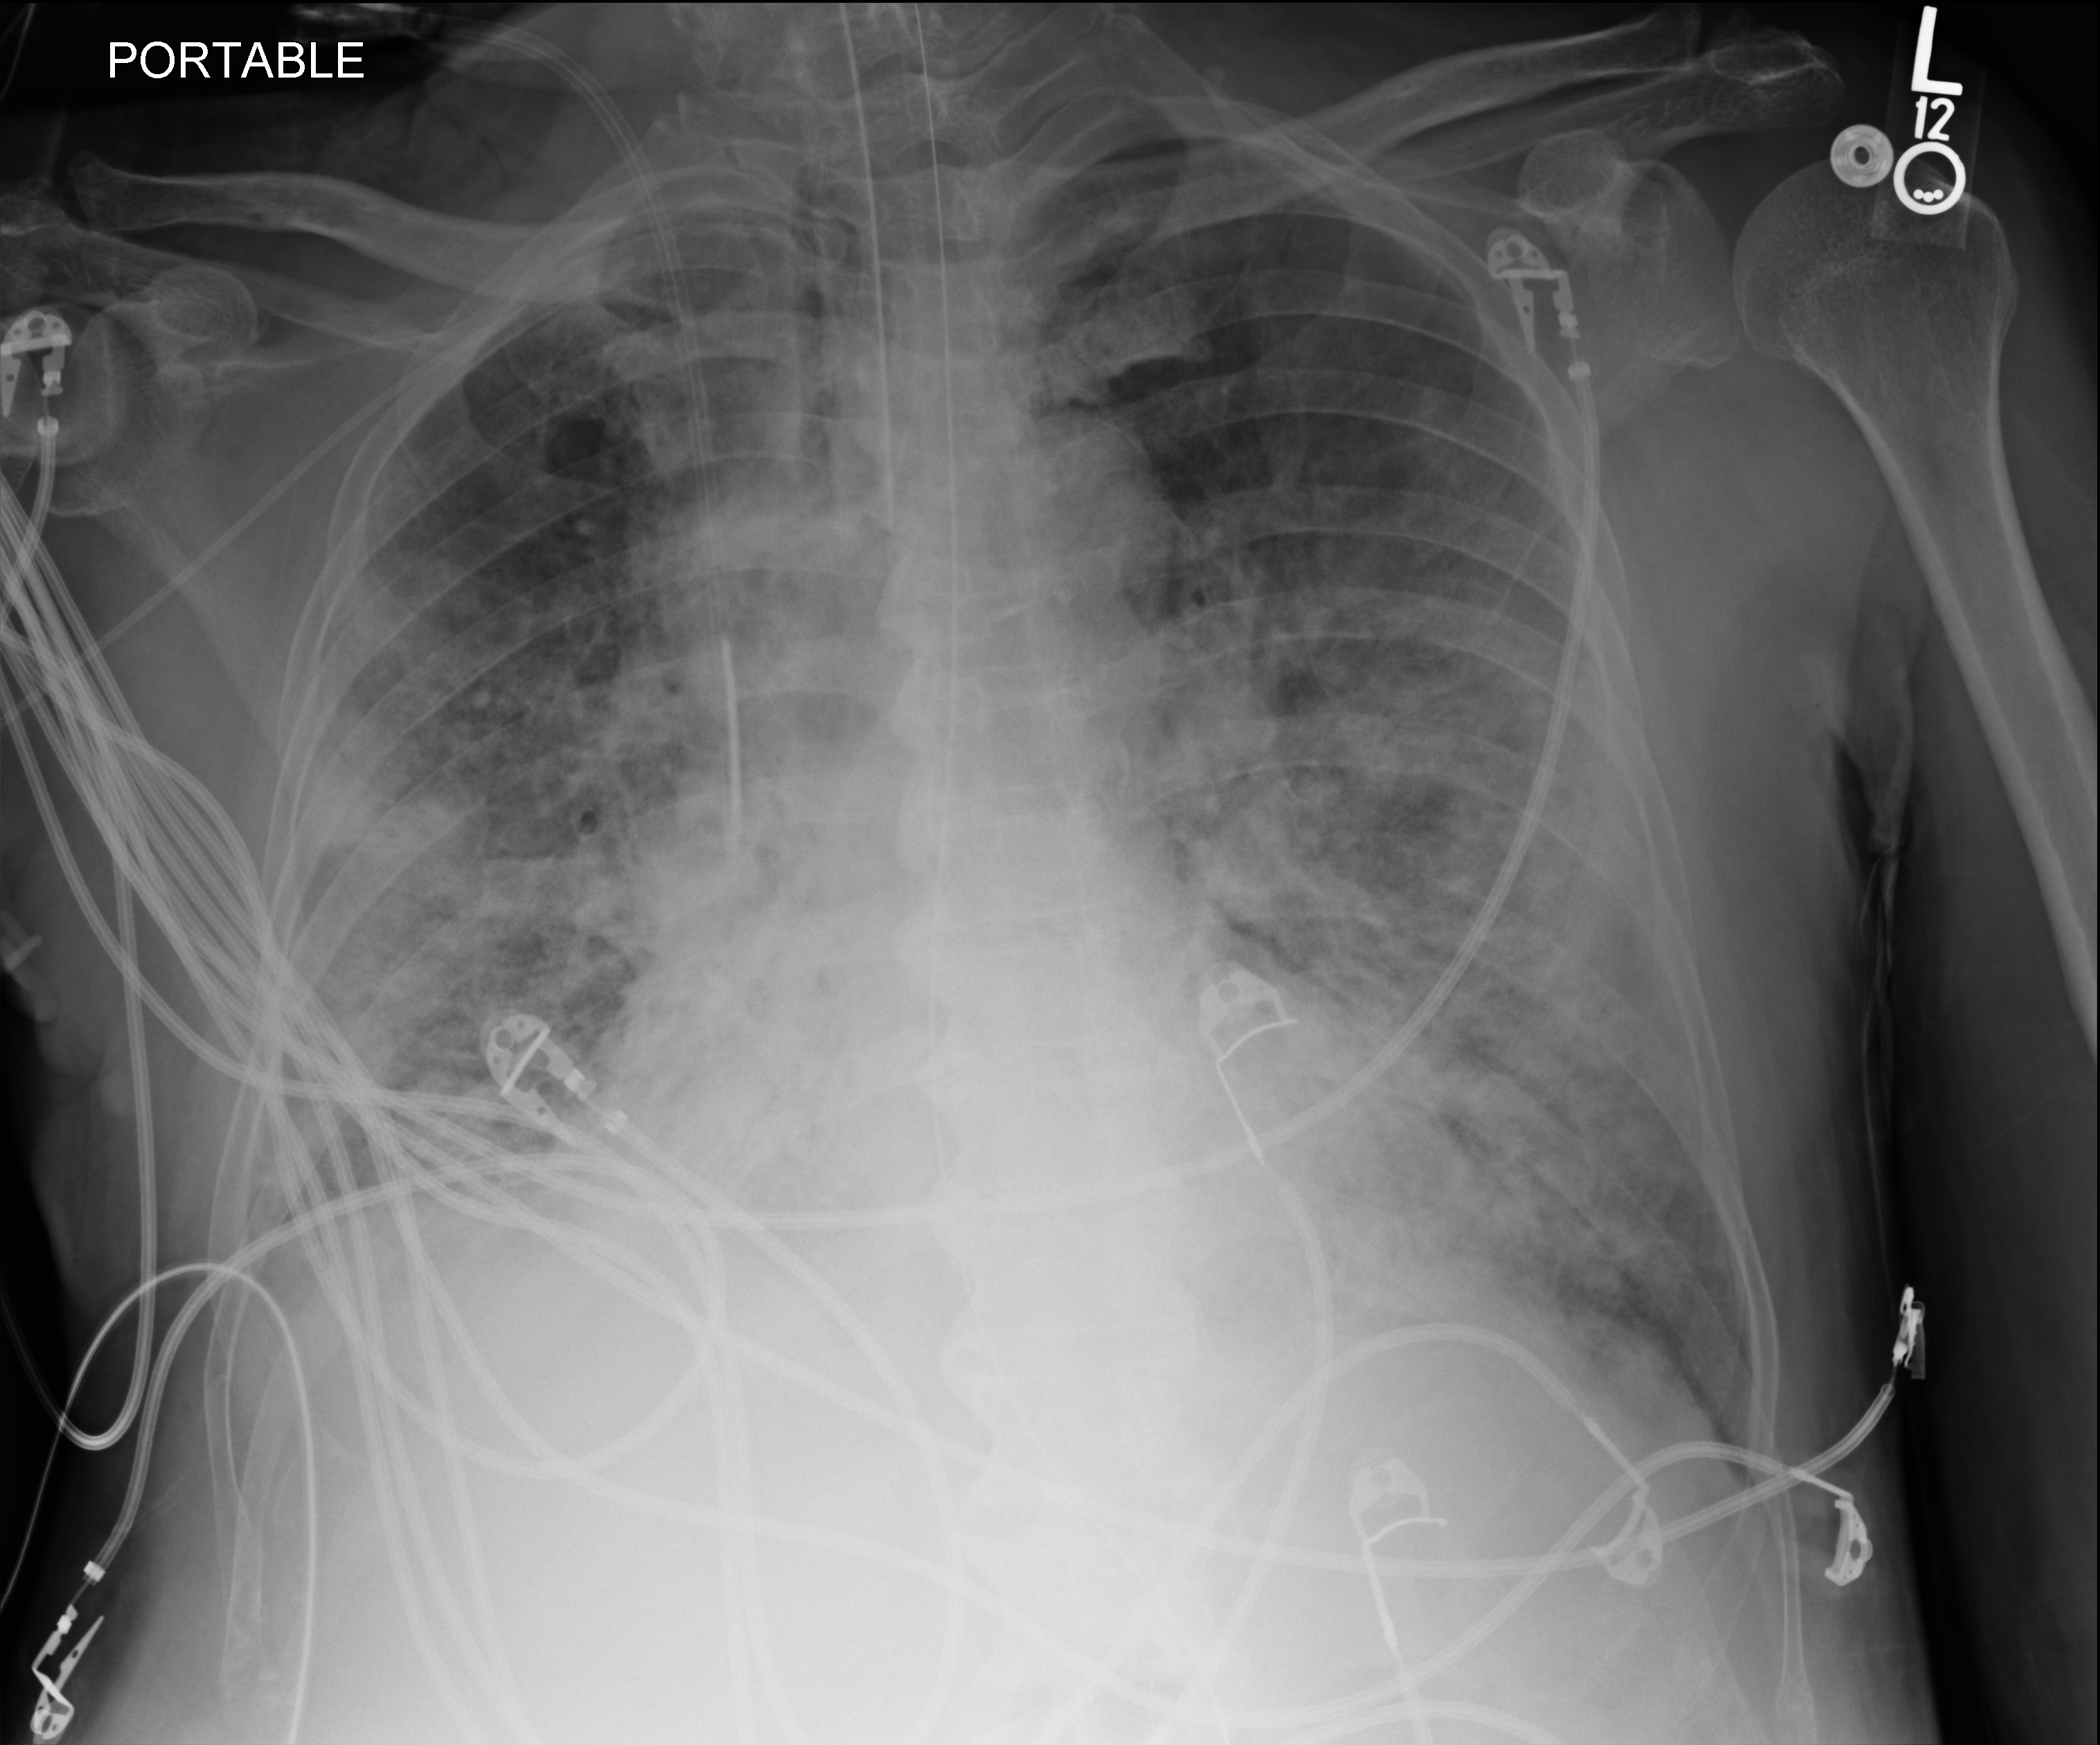
Bedside chest radiograph (computed radiography); anteroposterior (AP) projection. Patient hospitalised with COVID-19; male, aged 60–74 years.
Hospital-stay facts (about this admission, not read from this image; timing relative to this image not recorded): mechanically ventilated during this hospital stay: yes; hypertension (admission record): yes; admitted to intensive care during this hospital stay: yes.